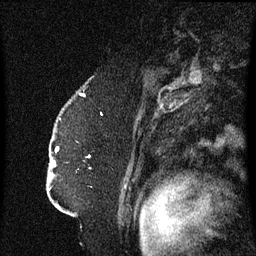
Breast MRI (dynamic contrast-enhanced), one sagittal slice. Position 47 of 60 along the scan axis. Dynamic contrast-enhanced series, image 2 of 3 at this slice position (ordered by acquisition). 1.5 T. TE 4.2 ms, TR 8.4 ms. 2.3 mm slice thickness. 256 × 256 image matrix, field of view 200 × 200 mm. Patient: female, 52 years. Case-level facts recorded for this patient, not image findings: setting: breast cancer imaged before/during neoadjuvant chemotherapy; receptor status: HR-positive, HER2-negative.
Outlined on this slice (semi-automatic segmentation, software-assisted and operator-edited):
- analysis volume of interest (the breast-tissue region the enhancement analysis was run in; not a lesion): bounding box <49,124,125,197> (left, top, right, bottom; pixels)
- tumour enhancement mask (voxels above the 70 % enhancement threshold inside the analysis volume of interest): <55,146,59,153>